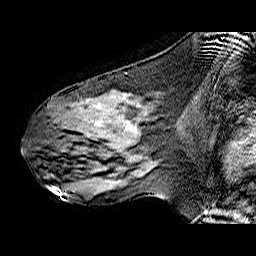
Breast MRI (dynamic contrast-enhanced), one sagittal slice. Slice 30 of 60 in the series (ordered by position). Dynamic contrast-enhanced series, time point 2 of 6 at this slice position (early post-contrast). 1.5 T. TE 6.3 ms, TR 32.9 ms. 4 mm slice thickness. 256 × 256 image matrix. Female patient. Case-level facts recorded for this patient, not image findings: setting: breast cancer imaged before/during neoadjuvant chemotherapy; receptor status: HER2-positive.
Structures marked on this image (semi-automatic segmentation, software-assisted and operator-edited):
- analysis volume of interest (the breast-tissue region the enhancement analysis was run in; not a lesion): box from (x=49, y=91) to (x=161, y=173) px
- tumour enhancement mask (voxels above the 100 % enhancement threshold inside the analysis volume of interest): (x=129, y=125)–(x=137, y=132)